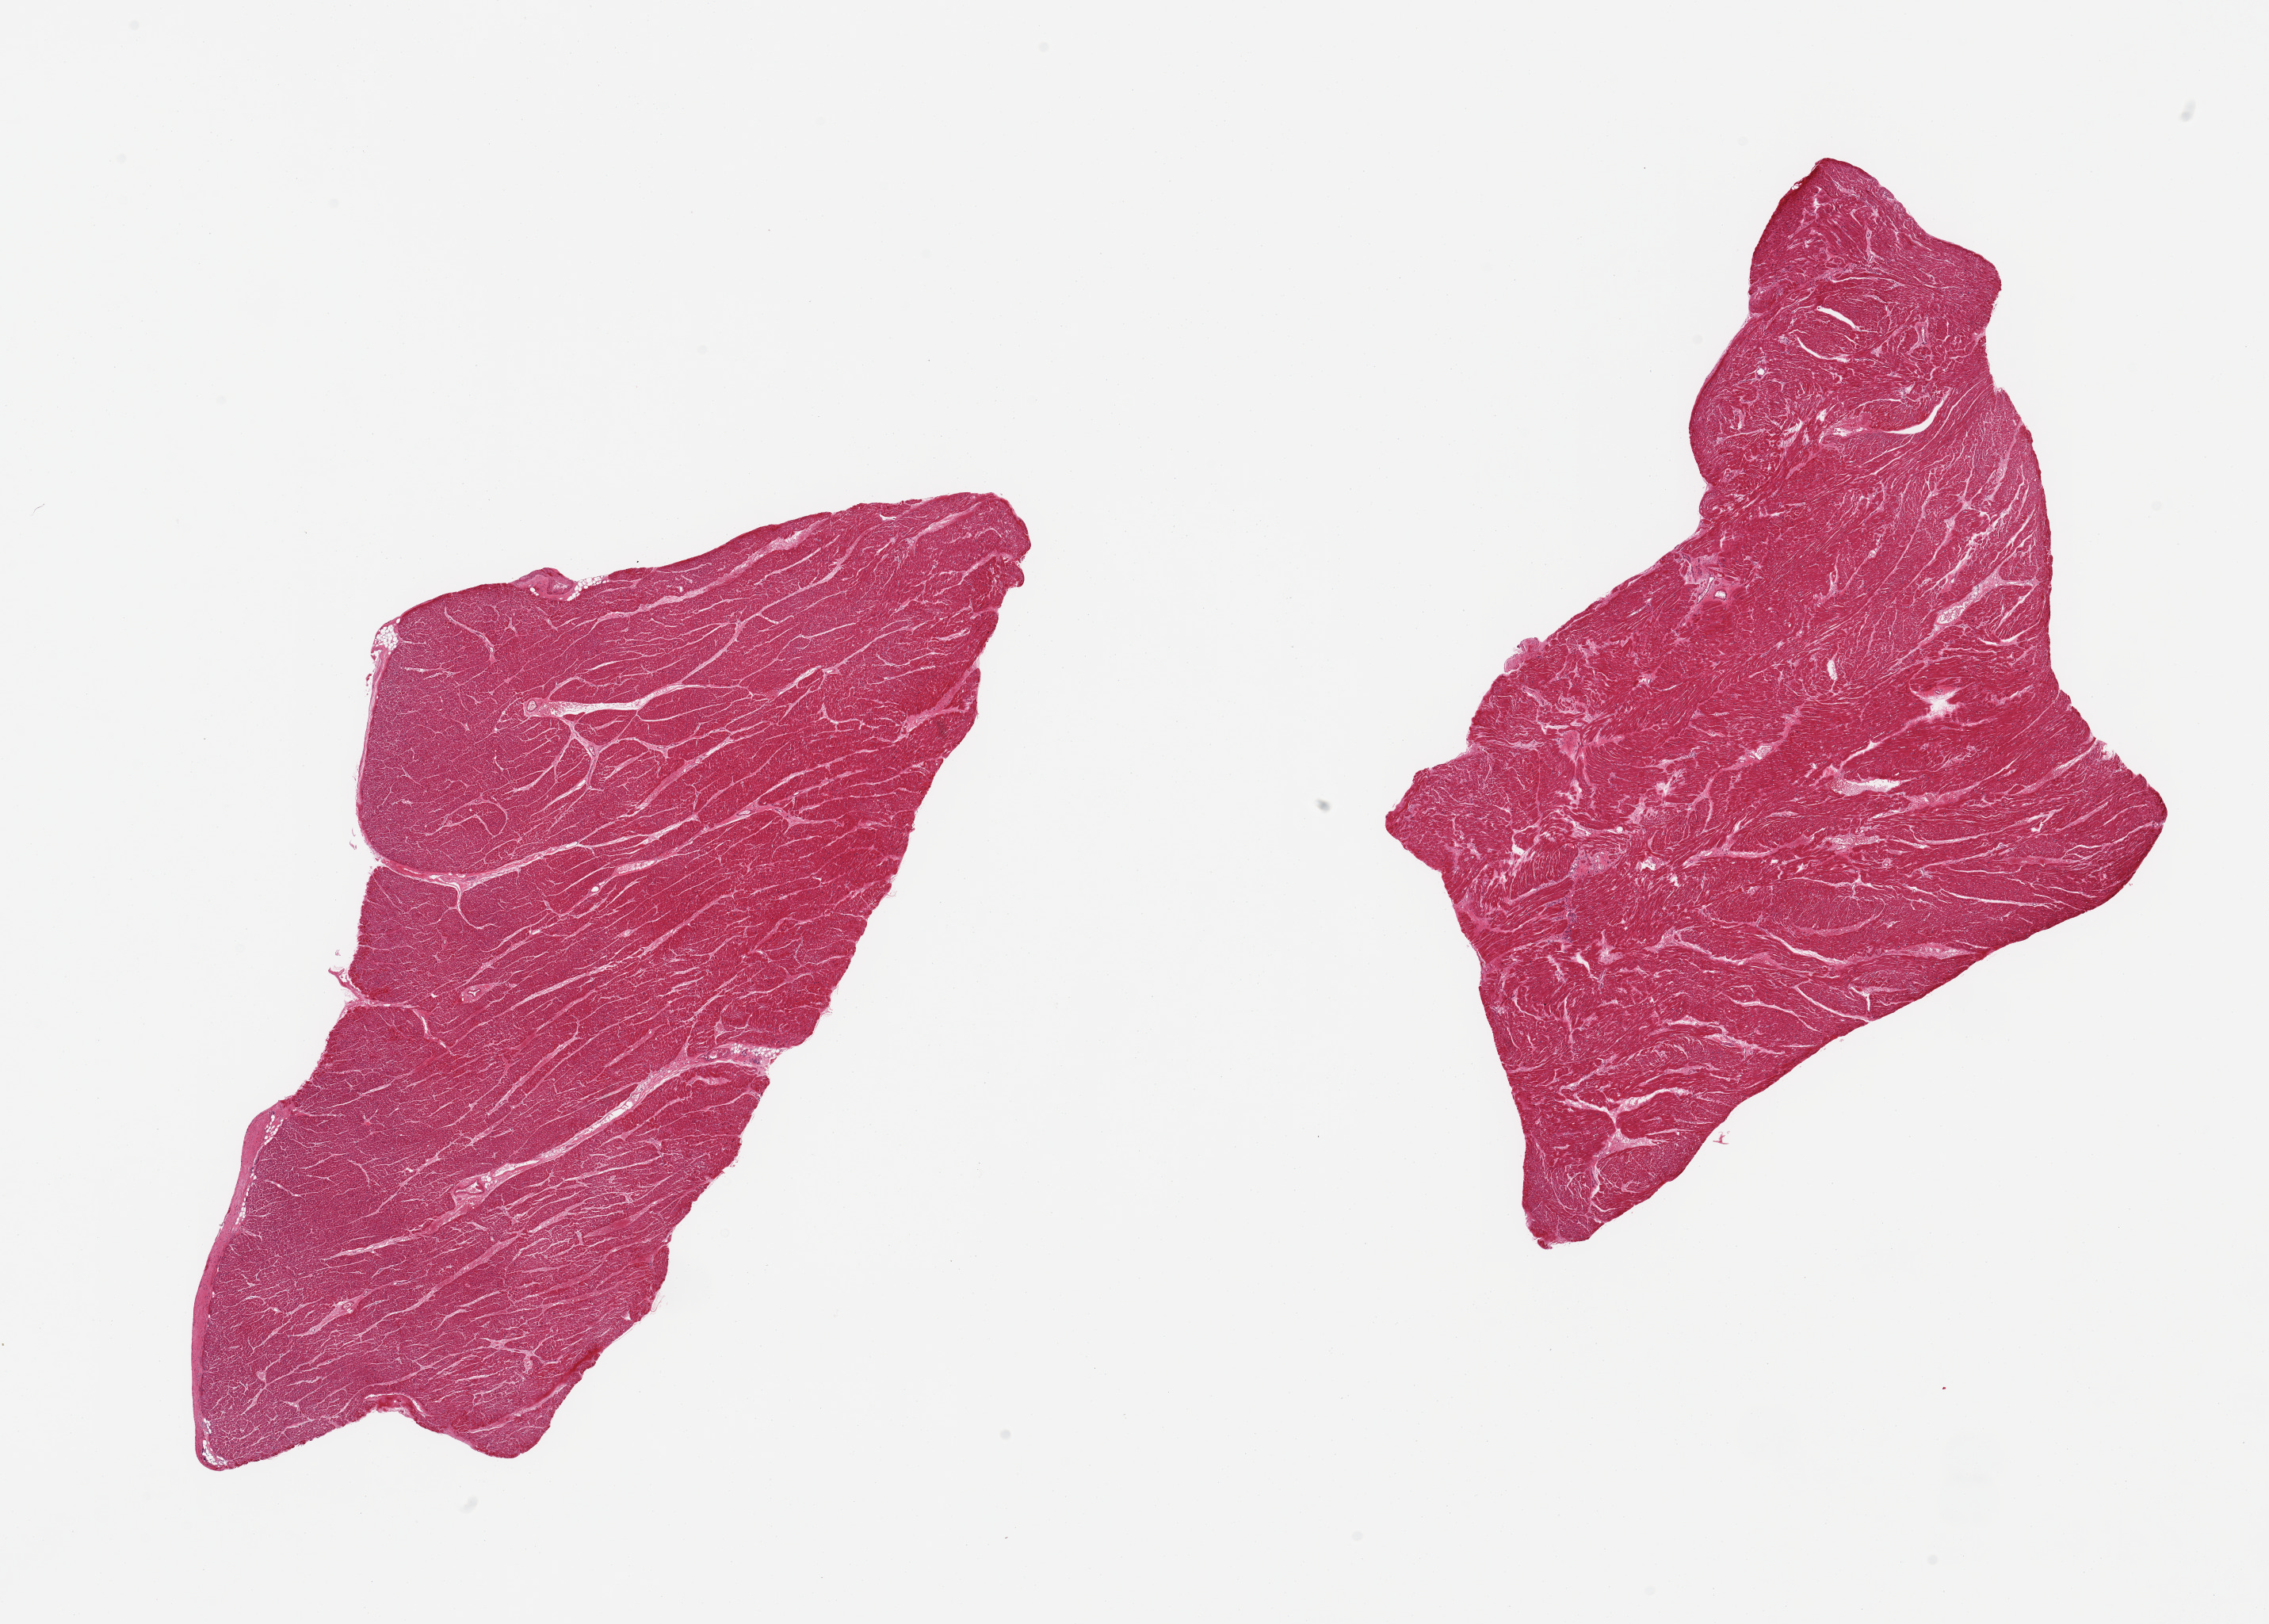
Whole-slide image, H&E stain — shown as a low-resolution overview of the whole scanned area (about 22.6 x 16.2 mm), PAXgene-fixed paraffin-embedded (PFPE) section, target tissue: heart, donor tissue sample.
* review note (as recorded): 2 pieces, minimal chronic ischemic change/interstitial fibrosis